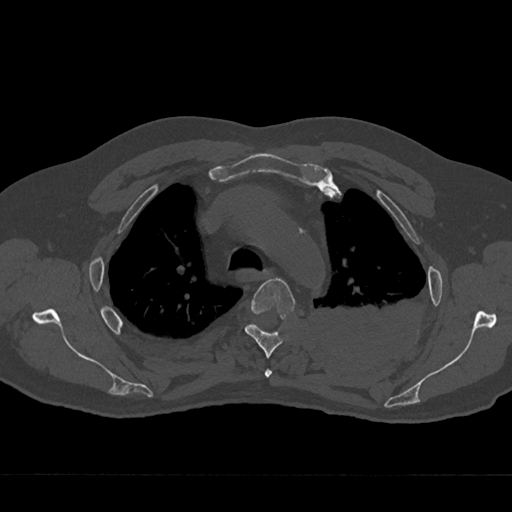
CT including the spine, one axial slice. Slice 520 of 797 in the series (ordered by position). Reconstruction kernel Br40s/3. 120 kVp. Bone window (W 1800 / L 400 HU). 0.5 mm slice thickness. 512 × 512 image matrix, field of view 377 × 377 mm. Male patient, age 75 years. From the clinical record (not read from this slice): primary cancer: renal; vertebrae with lytic lesions (as recorded): T4.
Structures marked on this image (semi-automatically segmented with operator editing):
- T3 vertebra: bounding box <264,369,272,378> (left, top, right, bottom; pixels)
- T4 vertebra: <244,278,295,358>